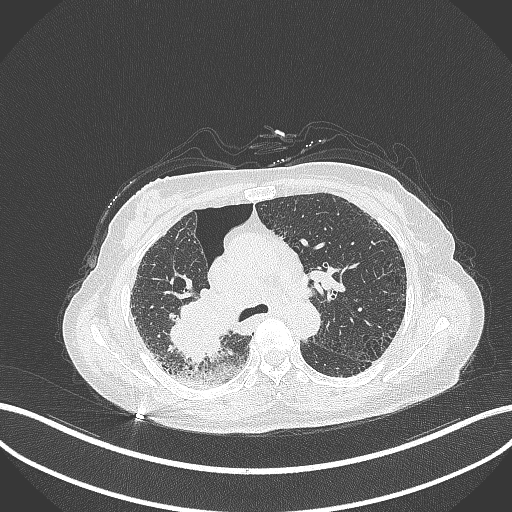
Chest CT, one axial slice; position 225 of 408 along the scan axis; reconstruction kernel B70f; lung window (W 1500 / L -600 HU); 1 mm slice thickness; 512 × 512 image matrix. Patient: female, 64 years. From the clinical record (not read from this slice): clinical TNM (as recorded): T3 N3 M0.
Outlined on this slice (bounding box drawn by a radiologist):
- lung tumour (recorded histology: squamous cell carcinoma): bounding box [x1, y1, x2, y2] px = [161, 277, 237, 366]